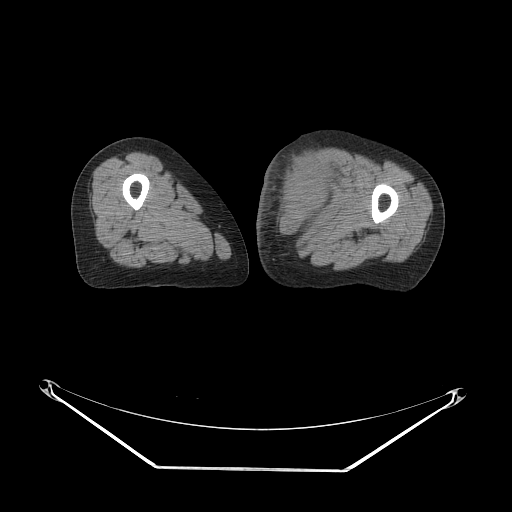
CT of an extremity soft-tissue mass (from a PET/CT study), one axial slice; position 41 of 91 along the scan axis; soft-tissue window (W 400 / L 40 HU); 3.75 mm slice thickness; 512 × 512 image matrix, field of view 500 × 500 mm. Female patient. From the clinical record (not read from this slice): histological type: pleomorphic leiomyosarcoma; grade: high; site of the primary tumour: left thigh.
Outlined on this slice (expert contour drawn on MRI and transferred to this co-registered scan by the dataset authors):
- gross tumour volume including surrounding oedema: bounding box [x1, y1, x2, y2] px = [267, 146, 344, 236]
- gross tumour volume (mass): [276, 146, 337, 225]